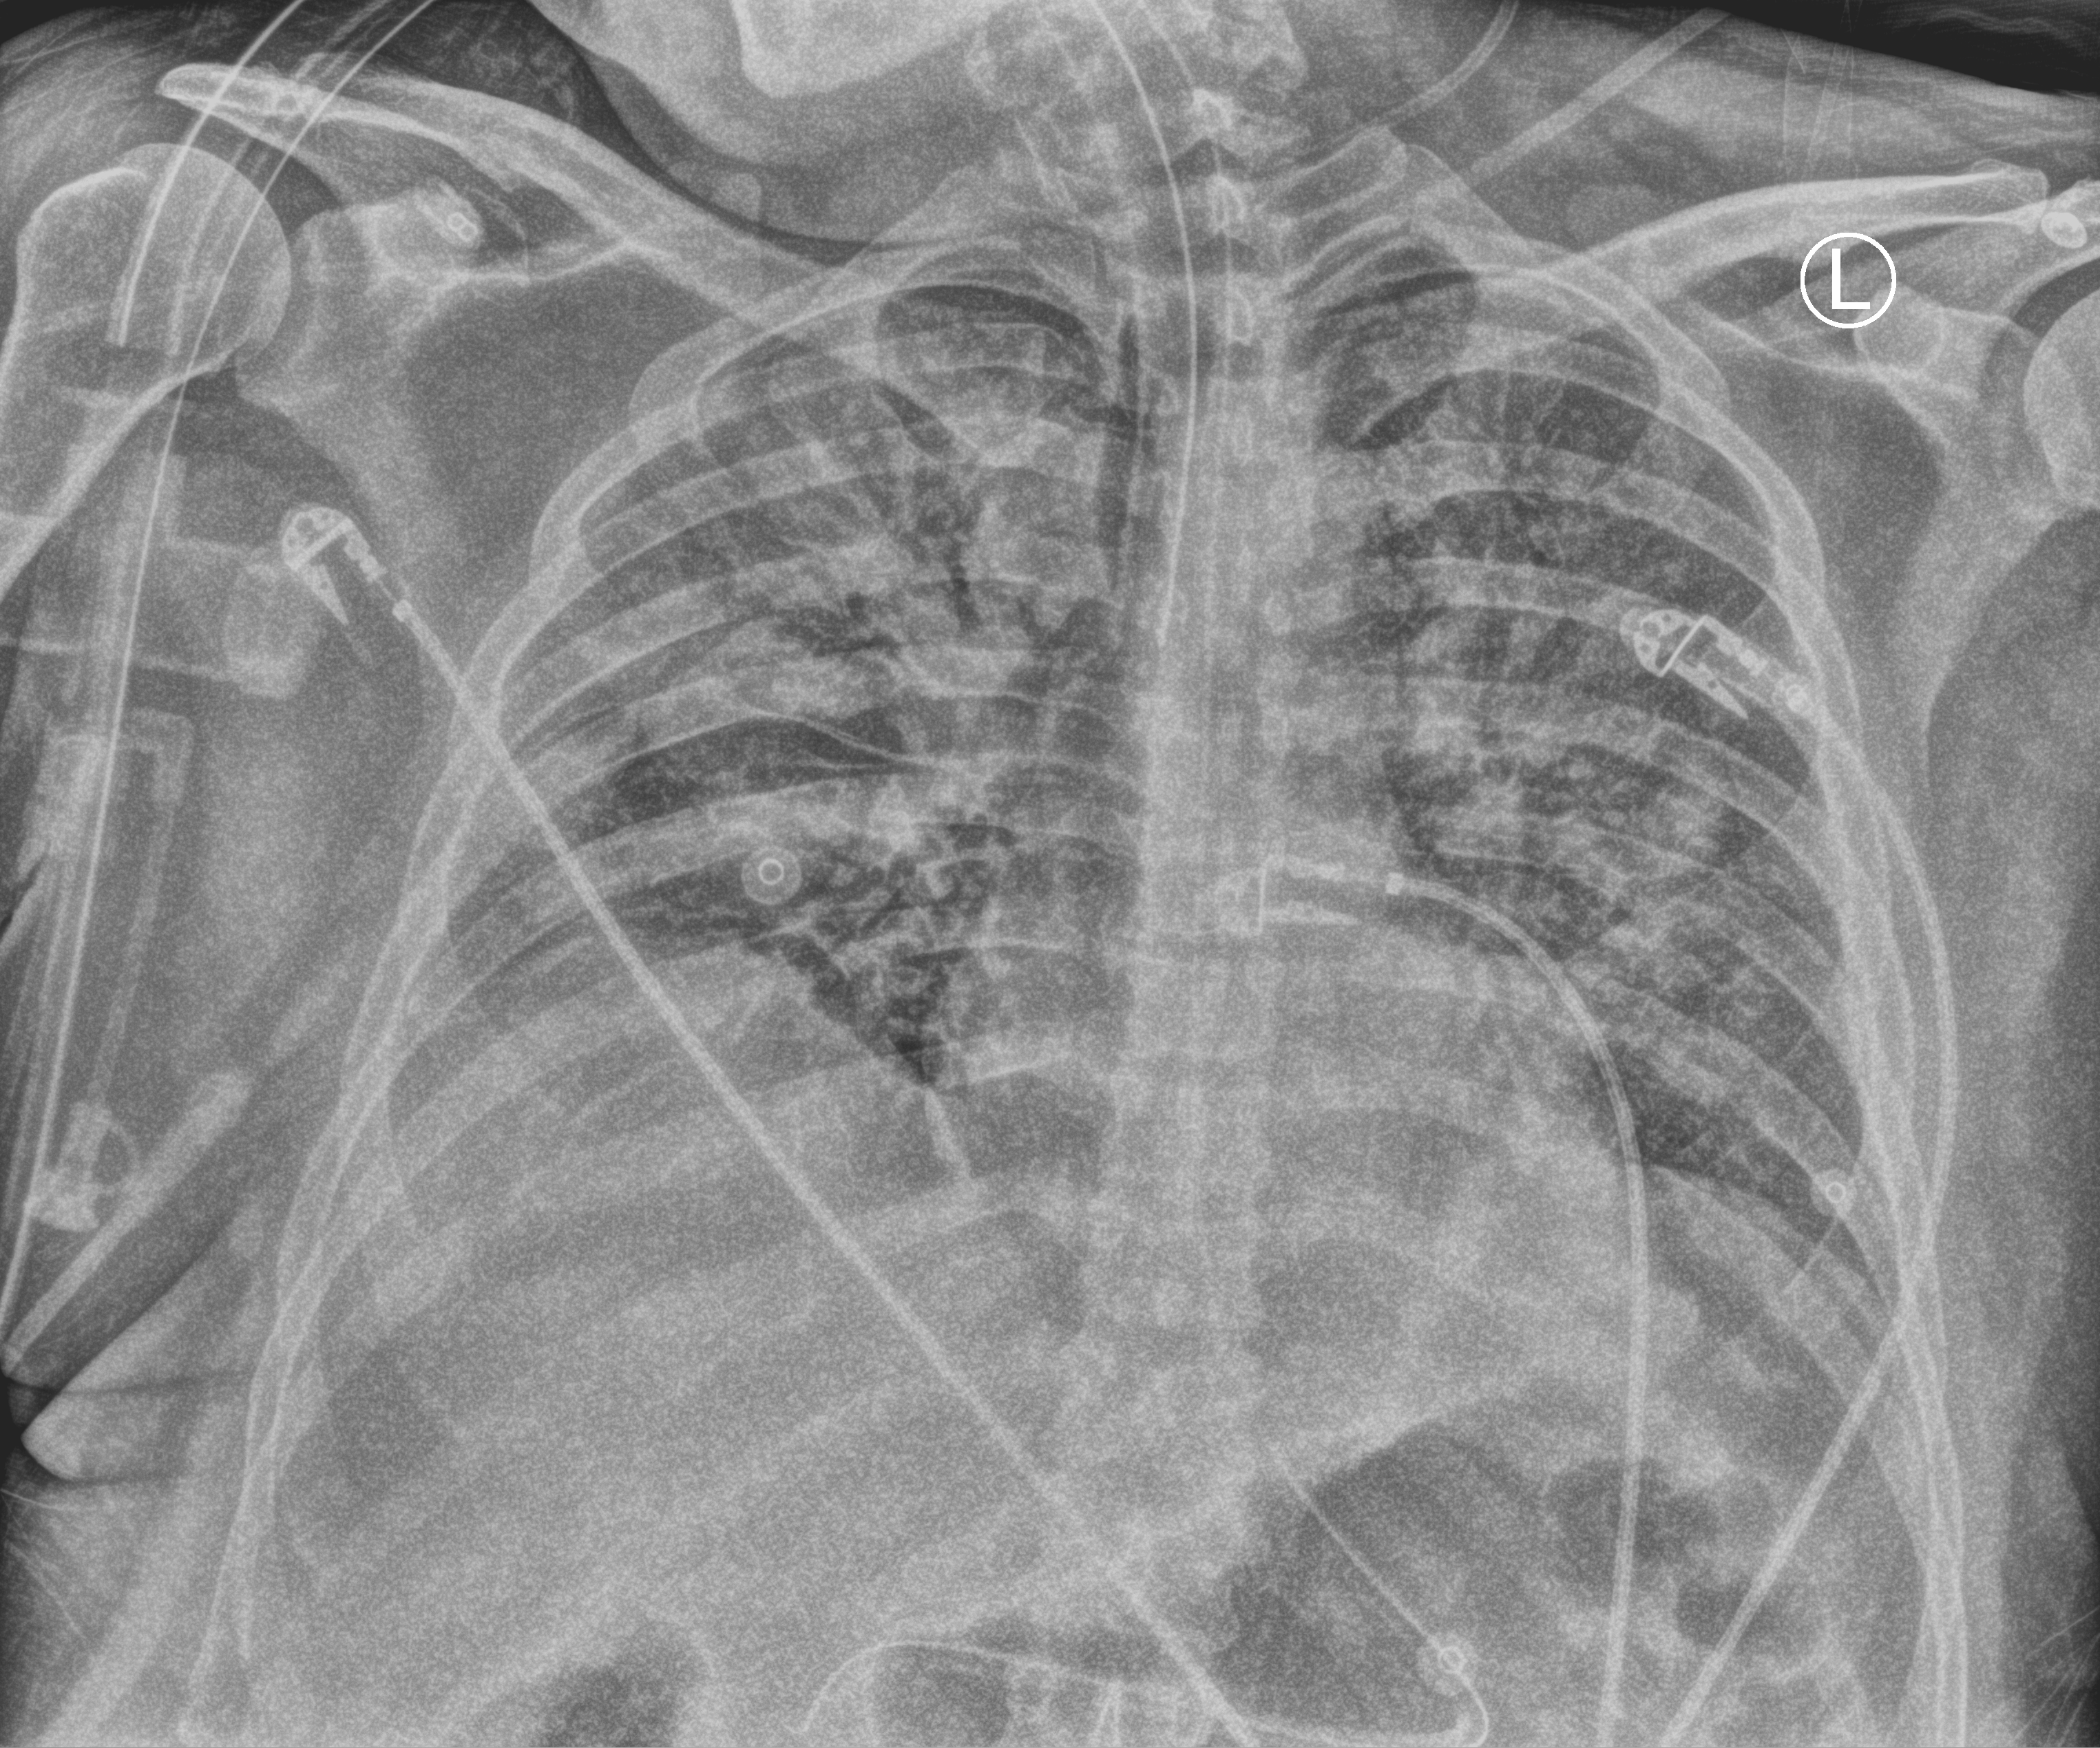
Portable chest radiograph; anteroposterior (AP) projection. Male patient hospitalised with COVID-19, age 18–59 years.
Hospital-stay facts (about this admission, not read from this image; timing relative to this image not recorded): chronic kidney disease (admission record): no; admitted to intensive care during this hospital stay: yes.